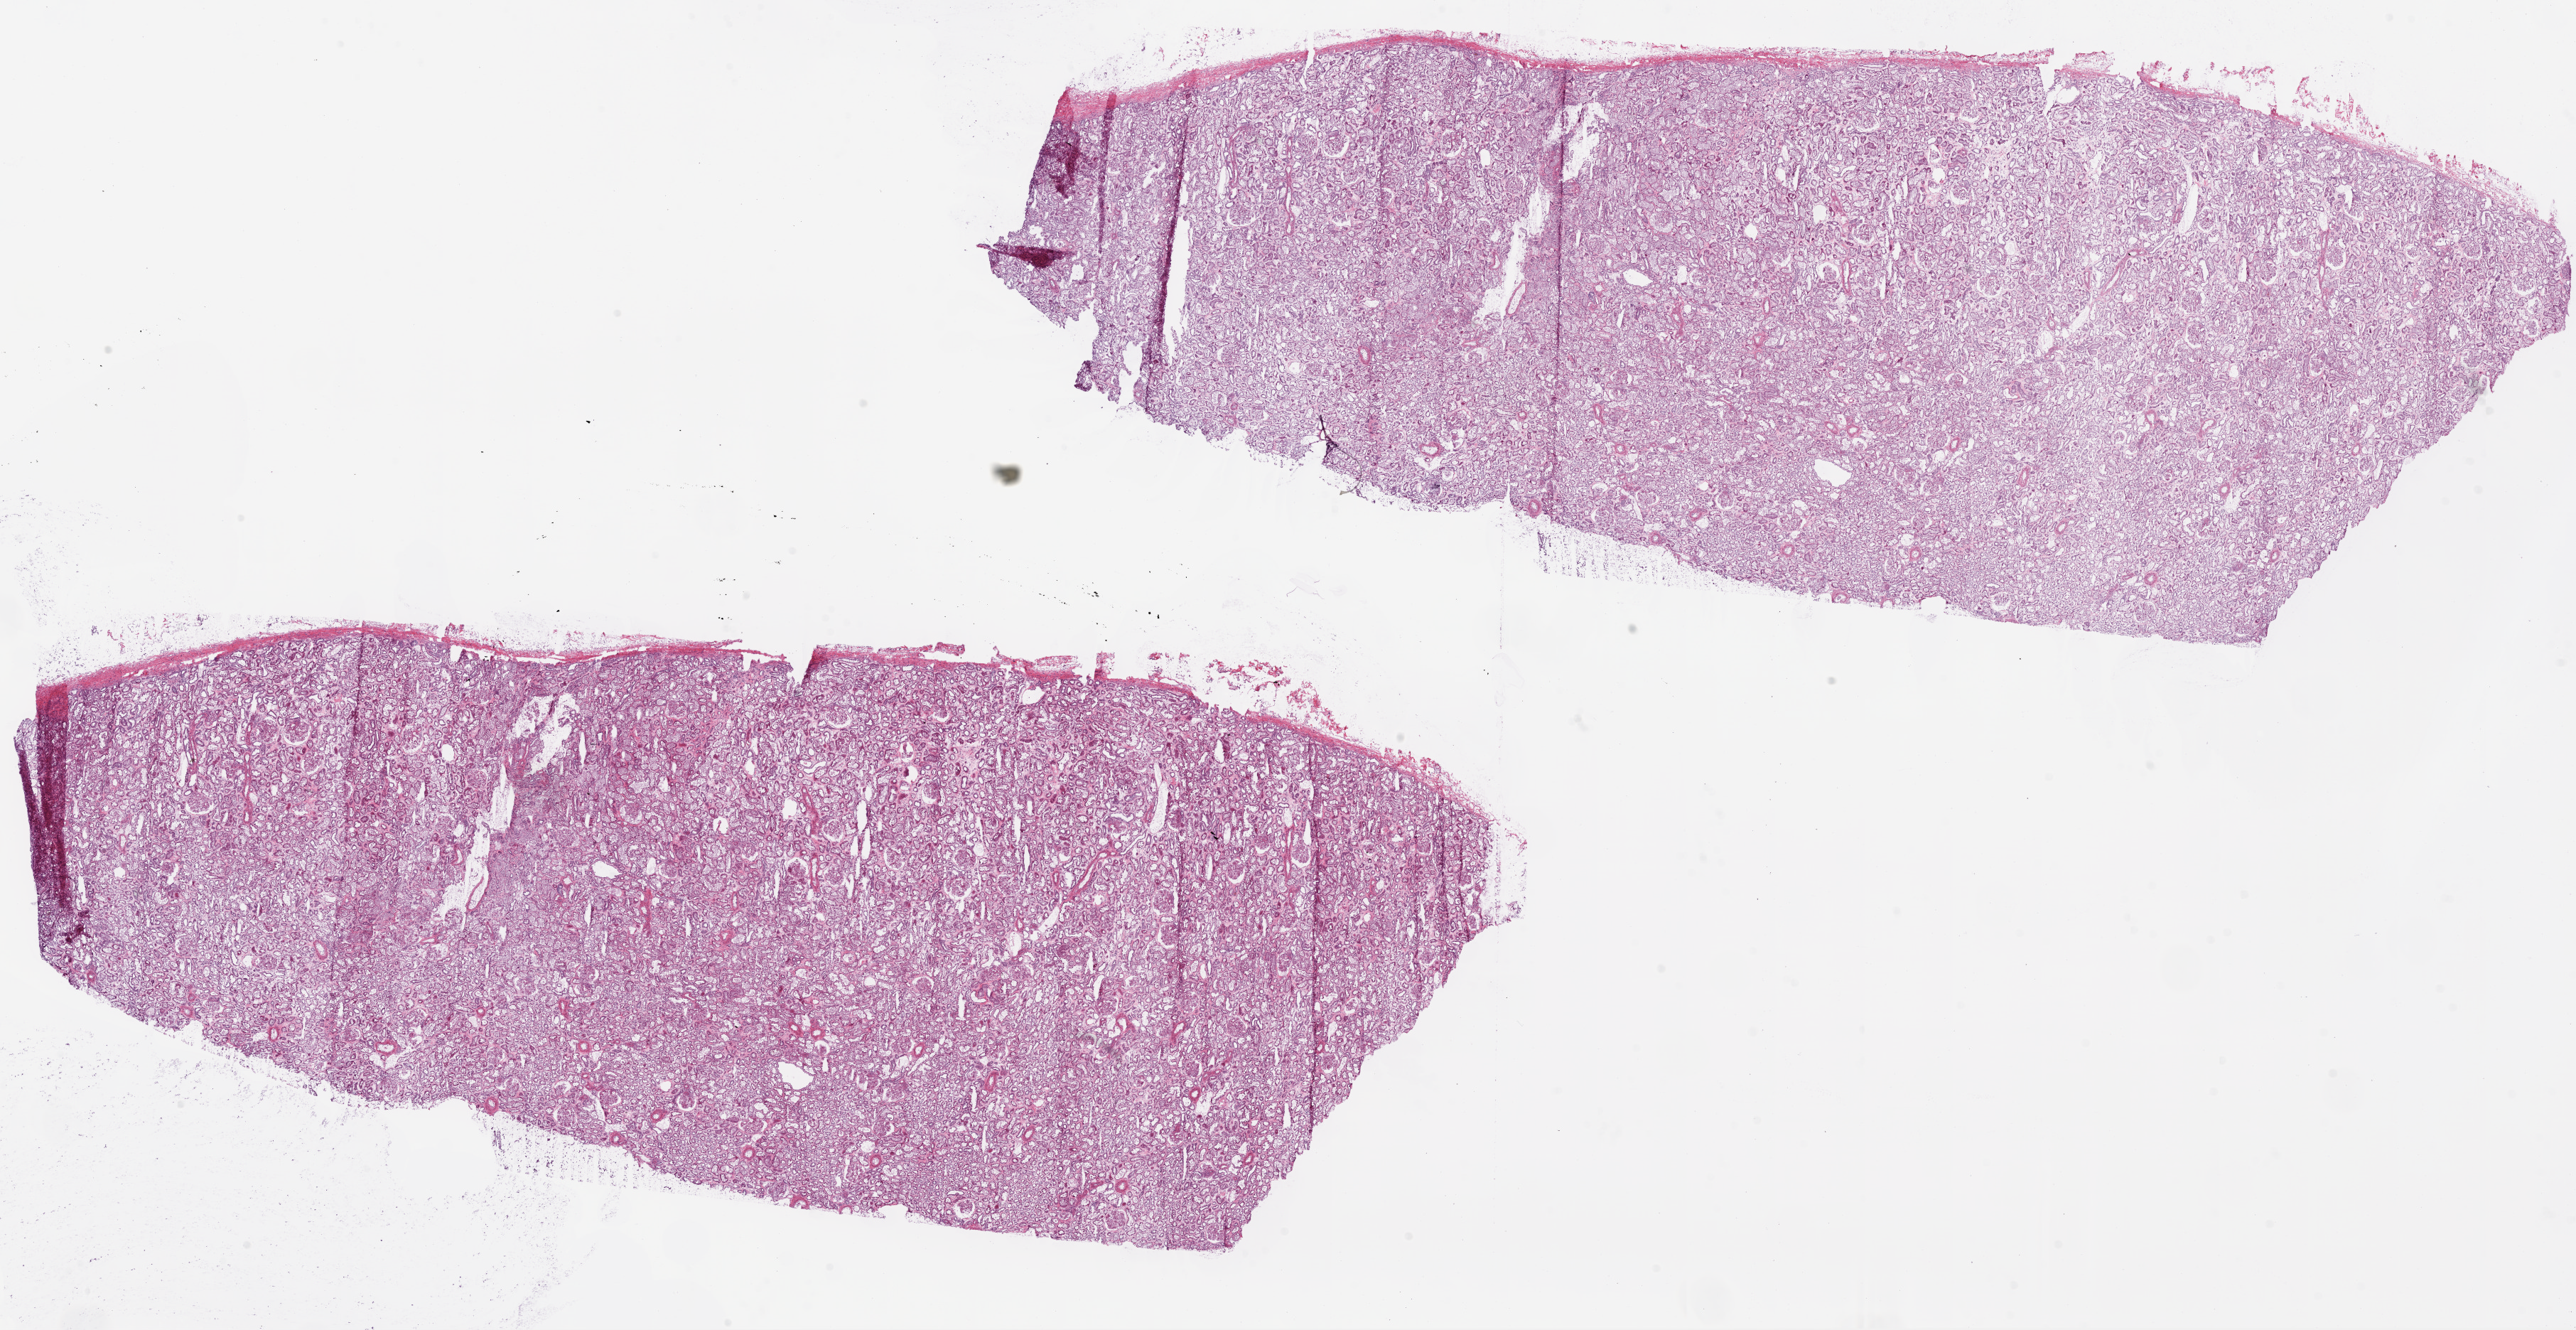
Hematoxylin and eosin (H&E) stained whole-slide image — low-resolution overview of the scanned area, about 29.1 x 15.0 mm (from a 20x scan). Frozen section from the top of the tissue portion. Sample: solid tissue normal (non-tumour tissue), kidney. Male, age 61 years at initial diagnosis.
This section: solid tissue normal (non-tumour) sample from the same patient. Patient diagnosis: Clear cell adenocarcinoma, NOS.